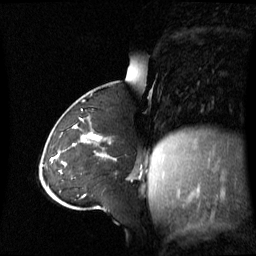
Breast MRI (dynamic contrast-enhanced), one sagittal slice; slice 24 of 60 in the series (ordered by position); dynamic contrast-enhanced series, image 2 of 3 at this slice position (ordered by acquisition); 1.5 T; TE 4.2 ms, TR 8.4 ms; 2.8 mm slice thickness; 256 × 256 image matrix, field of view 270 × 270 mm. Patient: female, 43 years. Case-level facts recorded for this patient, not image findings: setting: breast cancer imaged before/during neoadjuvant chemotherapy; receptor status: triple-negative.
Outlined on this slice (semi-automatic segmentation, software-assisted and operator-edited):
- analysis volume of interest (the breast-tissue region the enhancement analysis was run in; not a lesion): bounding box (x1, y1, x2, y2) in pixels: (55, 124, 141, 173)
- tumour enhancement mask (voxels above the 70 % enhancement threshold inside the analysis volume of interest): (72, 125, 101, 146)